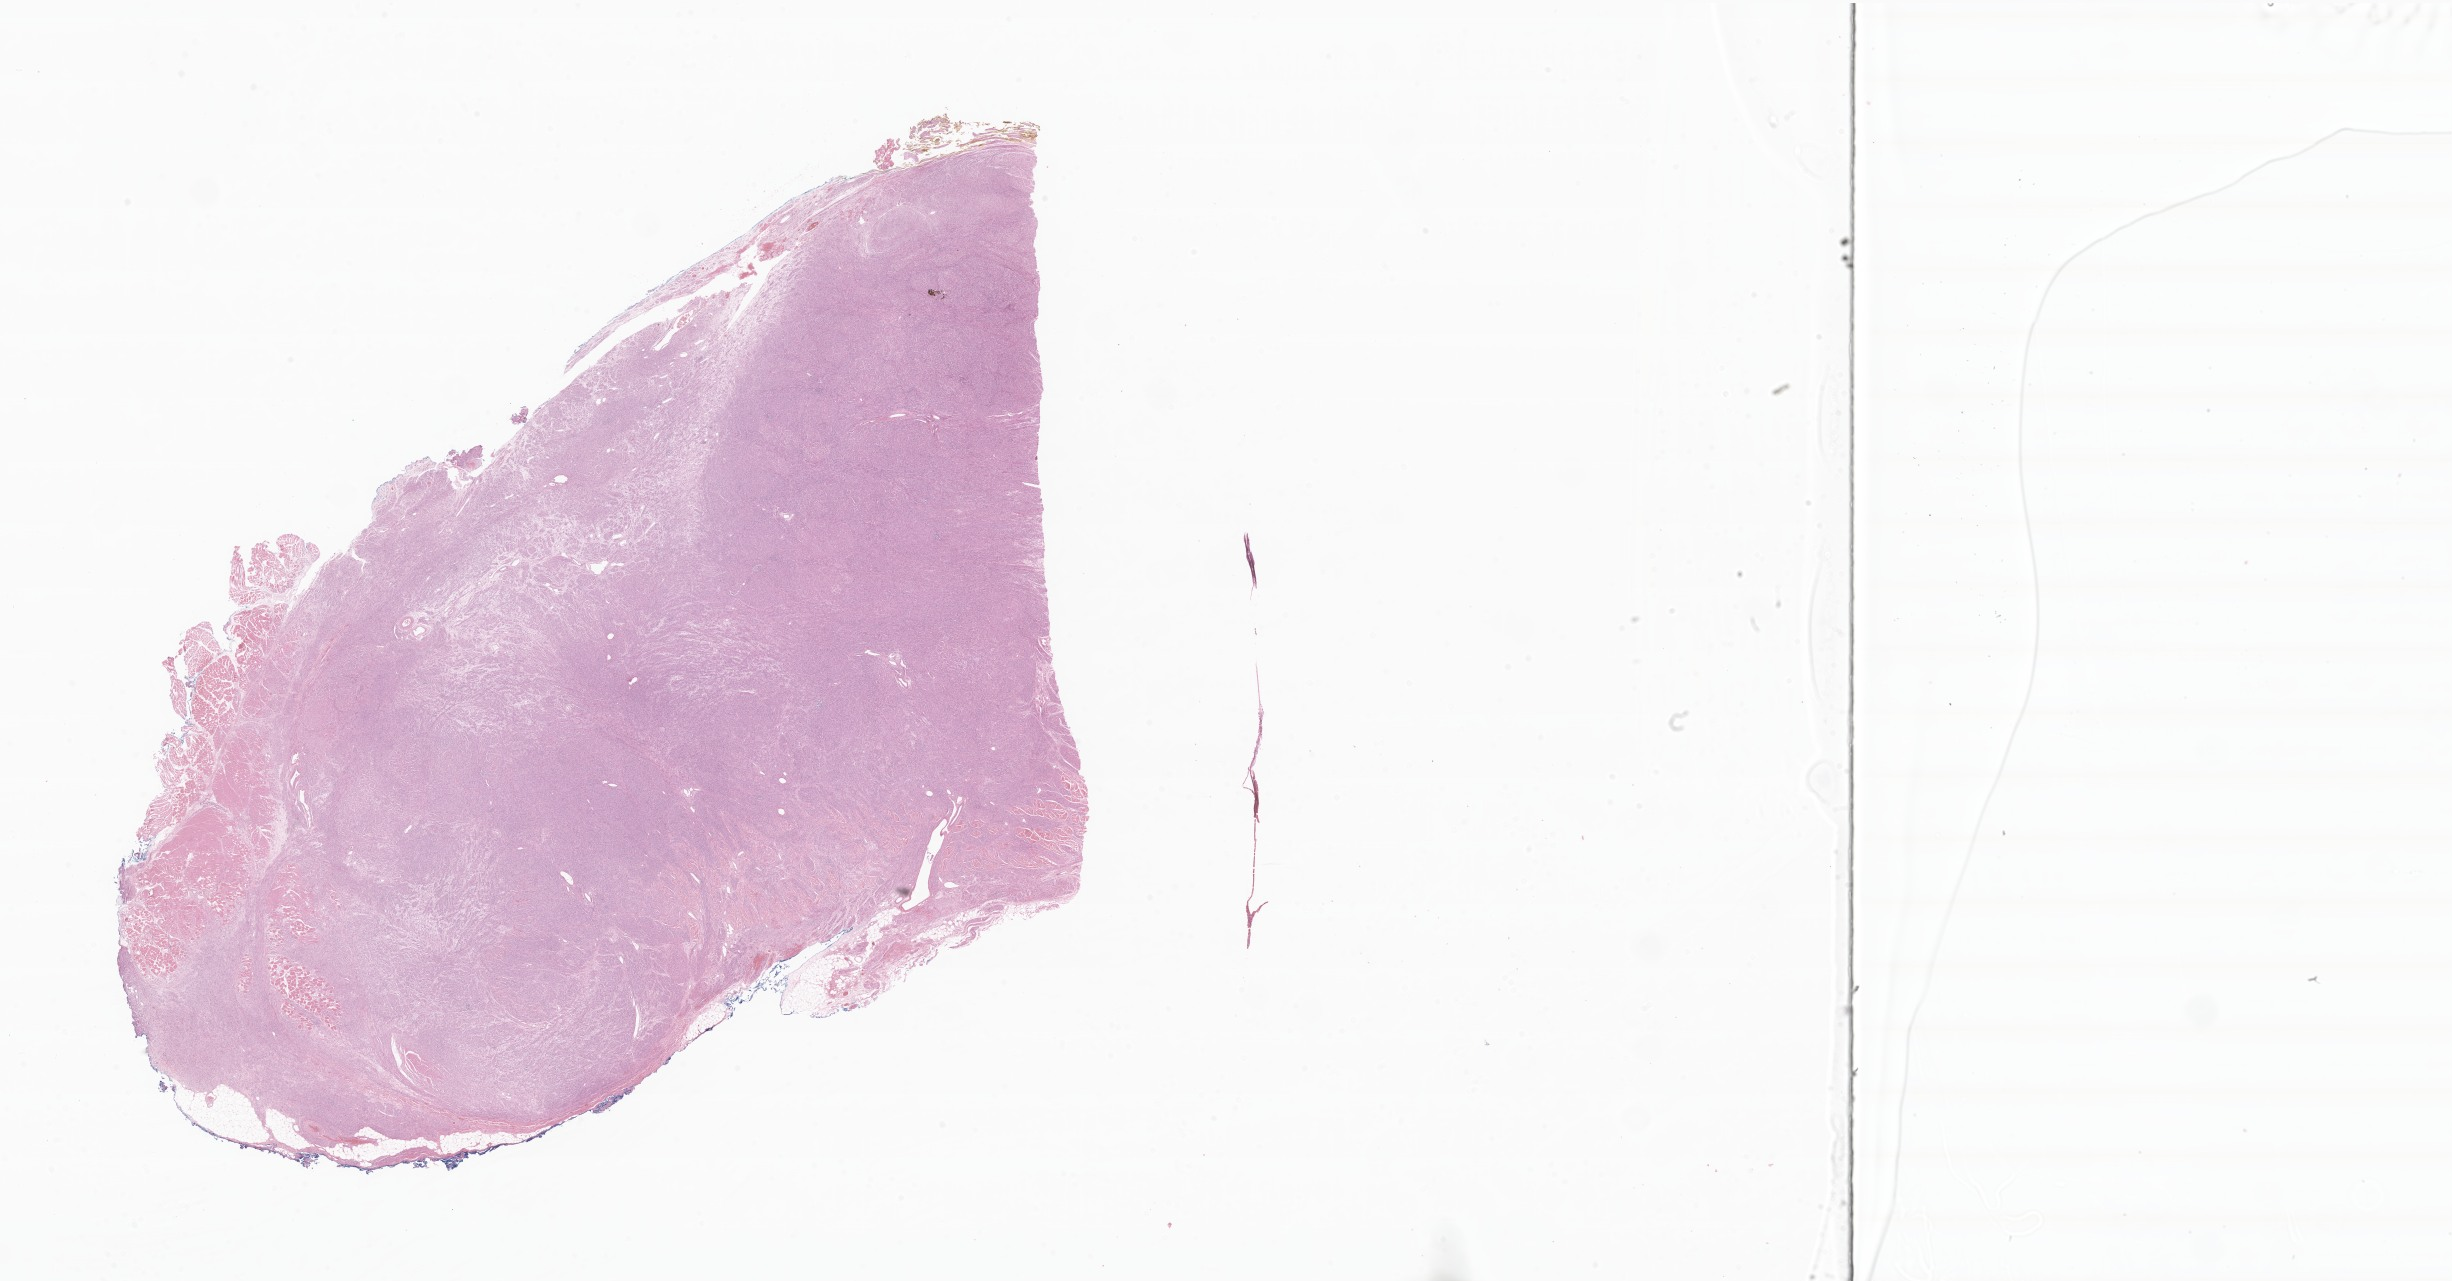
Whole-slide image, haematoxylin and eosin stain of tumor tissue from the soft tissue of trunk, low-resolution overview of the scanned area, about 41.3 x 21.6 mm. FFPE section. Male patient, age 530 days.
• diagnosis: Smooth muscle tumor of uncertain malignant potential